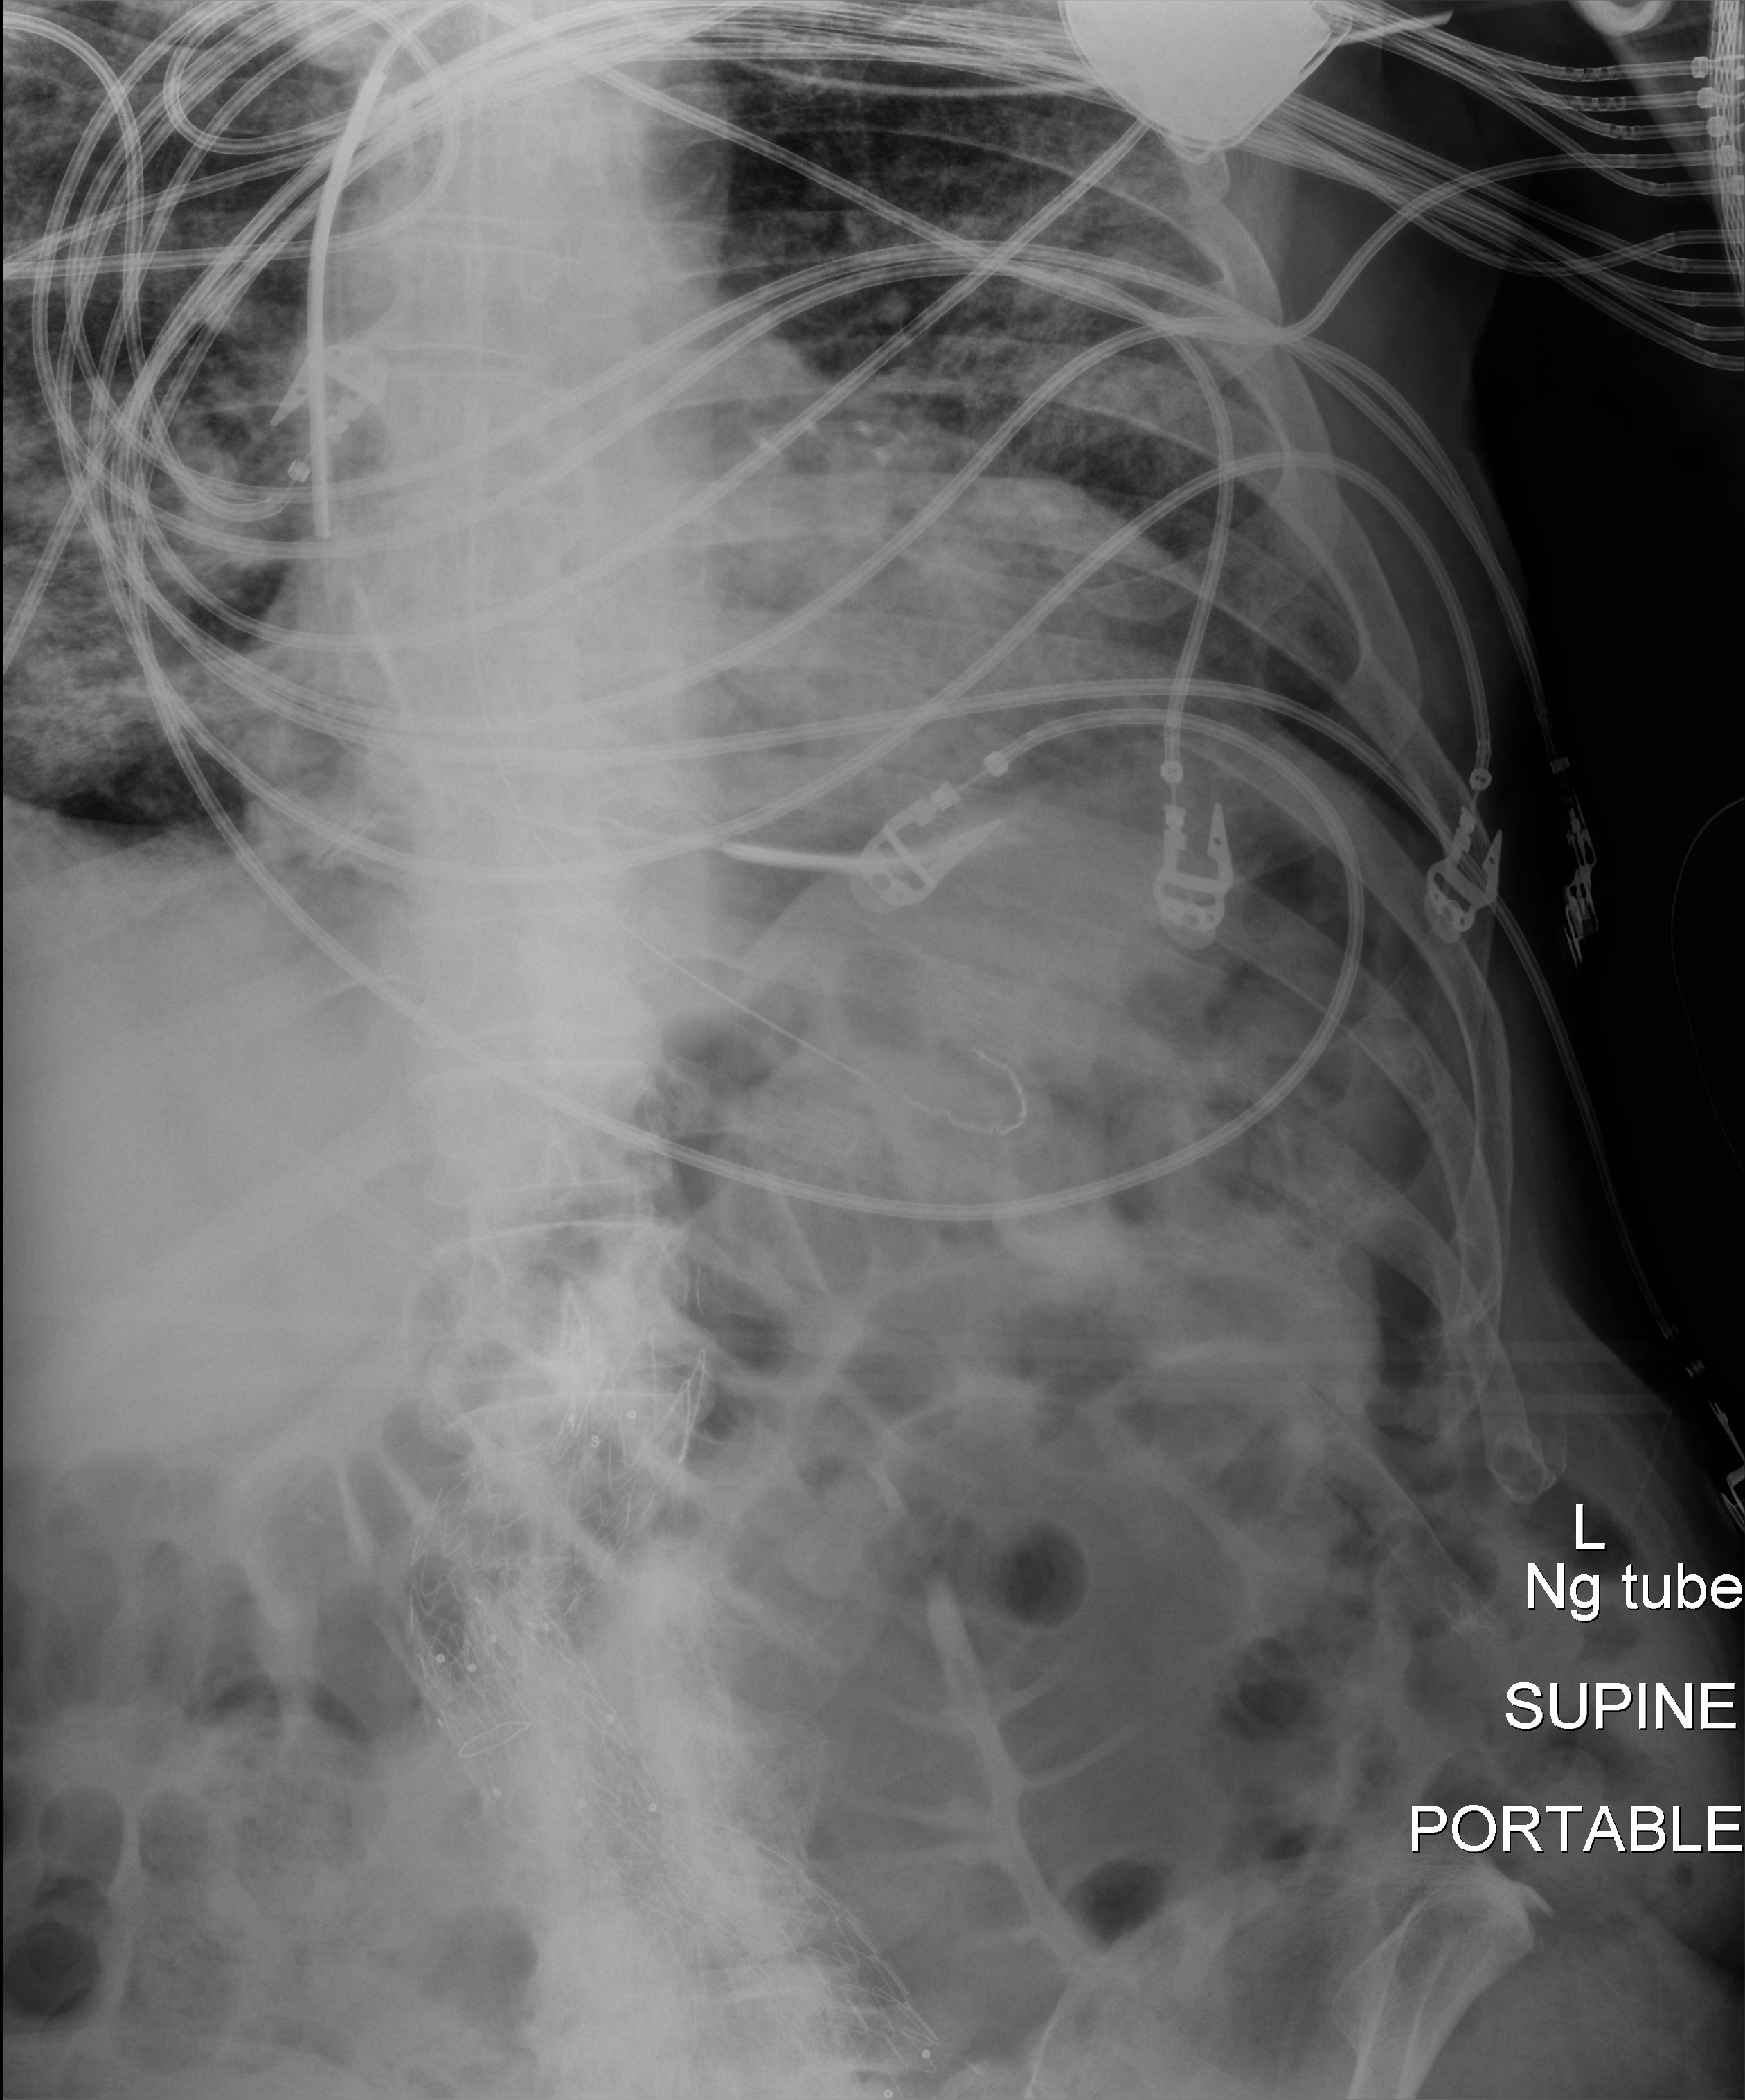
Bedside abdomen radiograph (digital radiography). Male patient hospitalised with COVID-19, age 60–74 years.
Hospital-stay facts (about this admission, not read from this image; timing relative to this image not recorded):
- admitted to intensive care during this hospital stay: yes
- length of hospital stay: 36 days